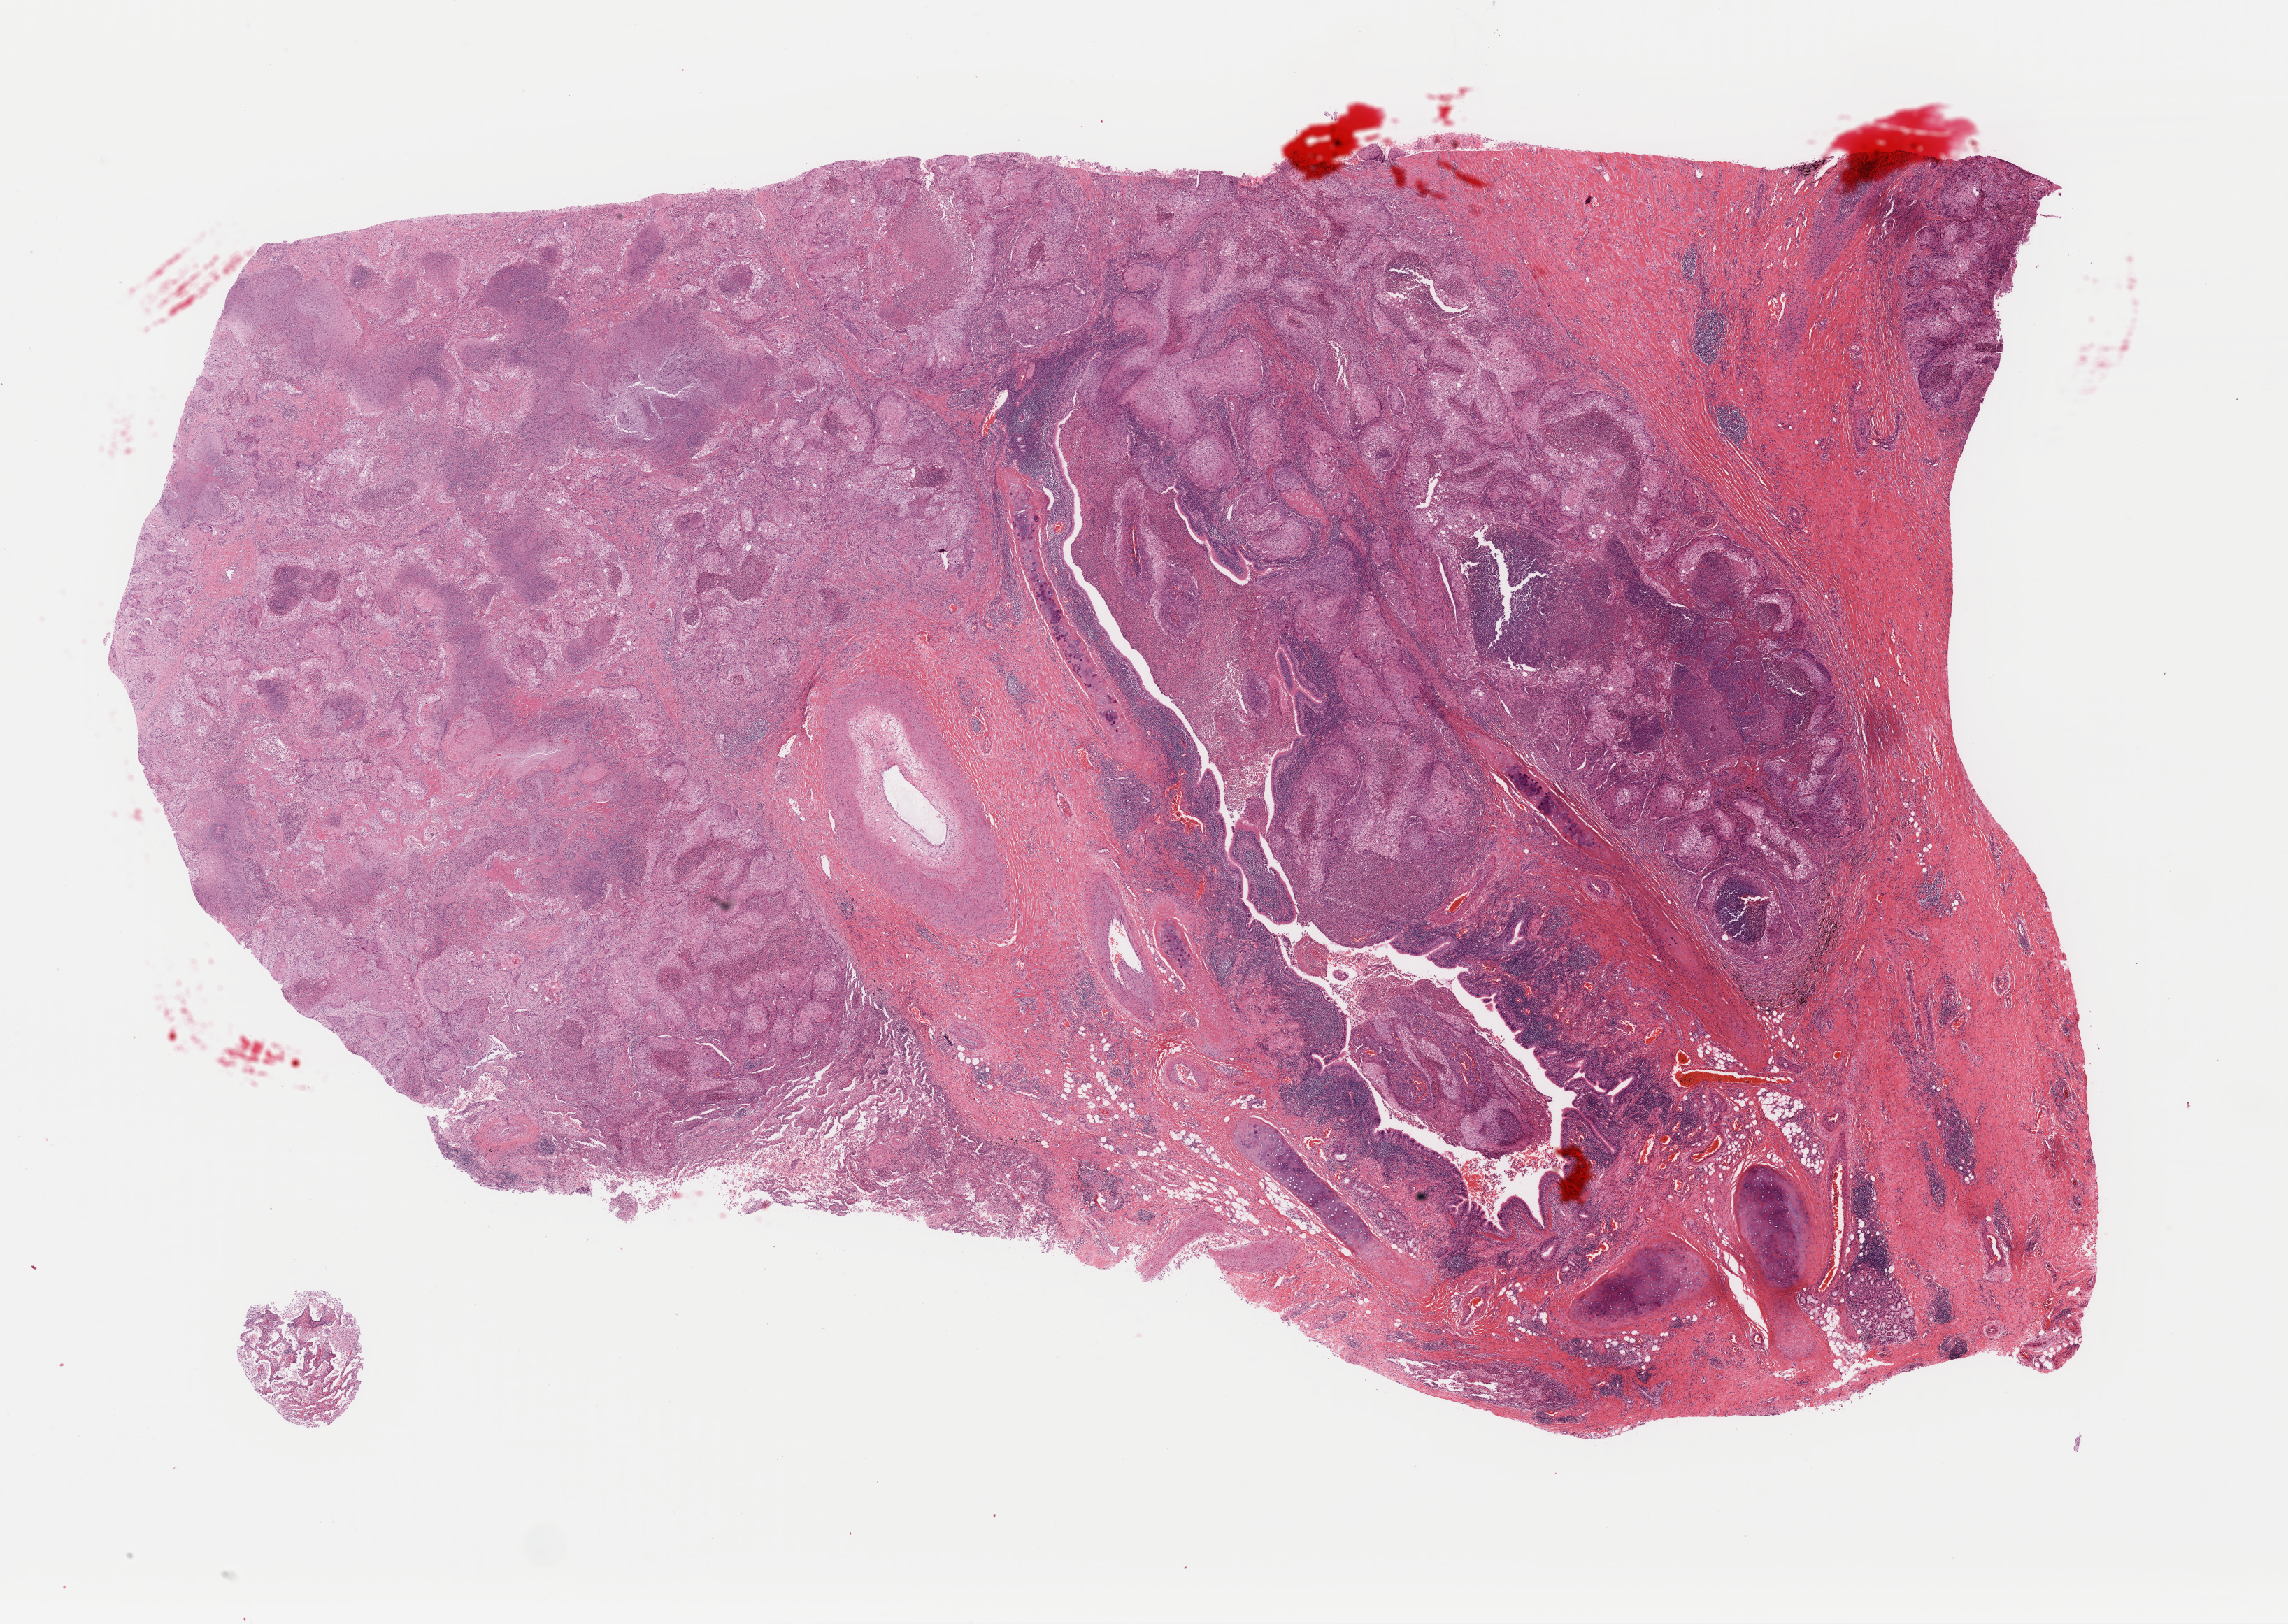
H&E-stained whole-slide image, low-resolution overview of the scanned area, about 25.8 x 18.3 mm (acquisition: 40x scan); formalin-fixed paraffin-embedded (FFPE) diagnostic section; lung, primary tumour sample. Male, age 84 years at initial diagnosis.
* histologic diagnosis: Squamous cell carcinoma, NOS (upper lobe, lung)
* AJCC pathologic stage: IIA